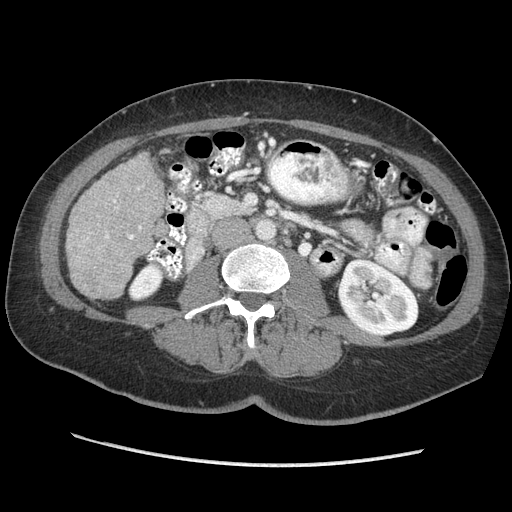
Contrast-enhanced abdominal CT (liver protocol), one axial slice; soft-tissue window (W 400 / L 40 HU); 2.5 mm slice thickness; 512 × 512 image matrix. Case-level facts recorded for this patient, not image findings: diagnosis: hepatocellular carcinoma (patient treated with transarterial chemoembolisation; whether this scan precedes or follows treatment is not stated here); TNM stage (as recorded): Stage-II; Child-Pugh class: A; tumour nodularity: multinodular; tumour size: 4 cm.
Structures marked on this image (semi-automatic segmentation, software-assisted and operator-edited):
- liver parenchyma outside the tumour (the mass and vessels are separate outlines, so this box may not span the whole liver): bounding box <66,152,166,298> (left, top, right, bottom; pixels)
- liver vessels: <105,187,142,240>